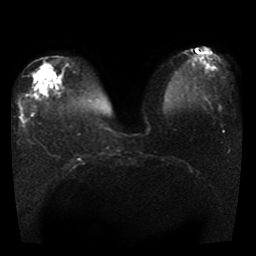
Breast MRI, one axial slice; position 13 of 41 along the scan axis; diffusion-weighted series; image 2 of 4 stored at this slice position (different b-values; order by instance number); 1.5 T; 5 mm slice thickness; 256 × 256 image matrix. Female patient.
Structures marked on this image (manually delineated by an expert):
- tumour on diffusion-weighted imaging: box from (x=40, y=87) to (x=44, y=93) px